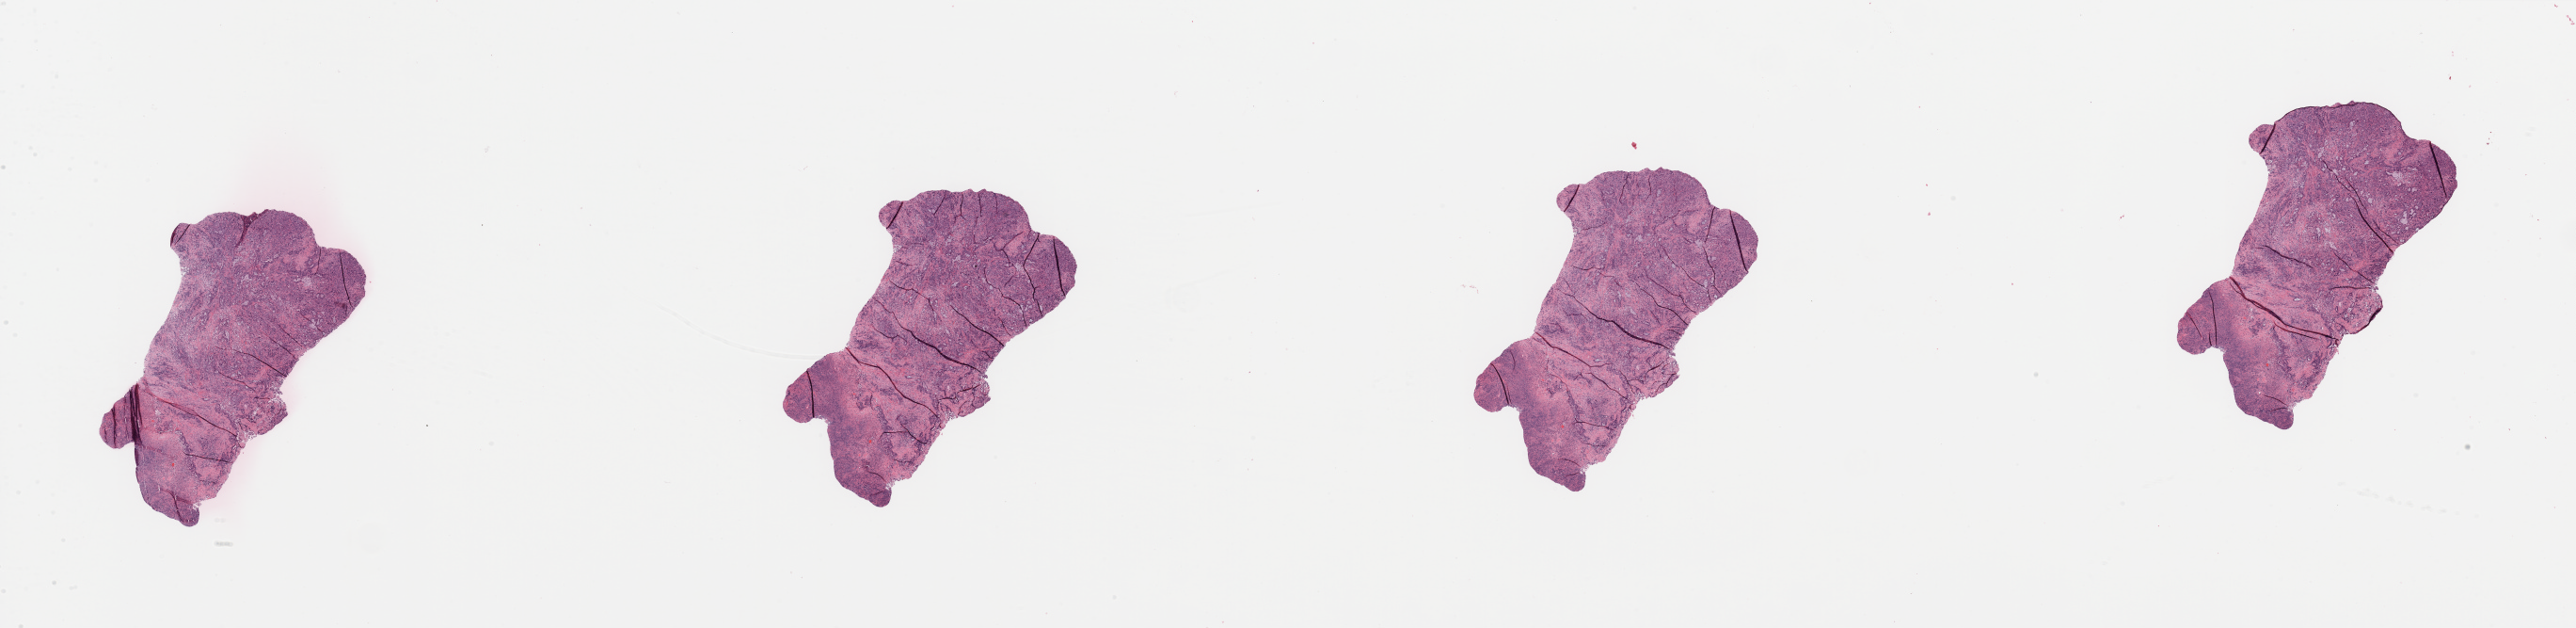
Whole-slide histology image, H&E-stained, a low-resolution overview of the entire scanned area, about 43.3 x 10.6 mm (from a 20x scan), tumour tissue sample, sampled site: pancreas. Female, 52 y/o. Histologic grade: G3 (poorly differentiated). Slide review estimates, as recorded: tumour nuclei 80%, necrosis 15%.
* primary tumour site (as recorded): head
* AJCC pathologic stage: IIB
* diagnosis: Infiltrating duct carcinoma, NOS